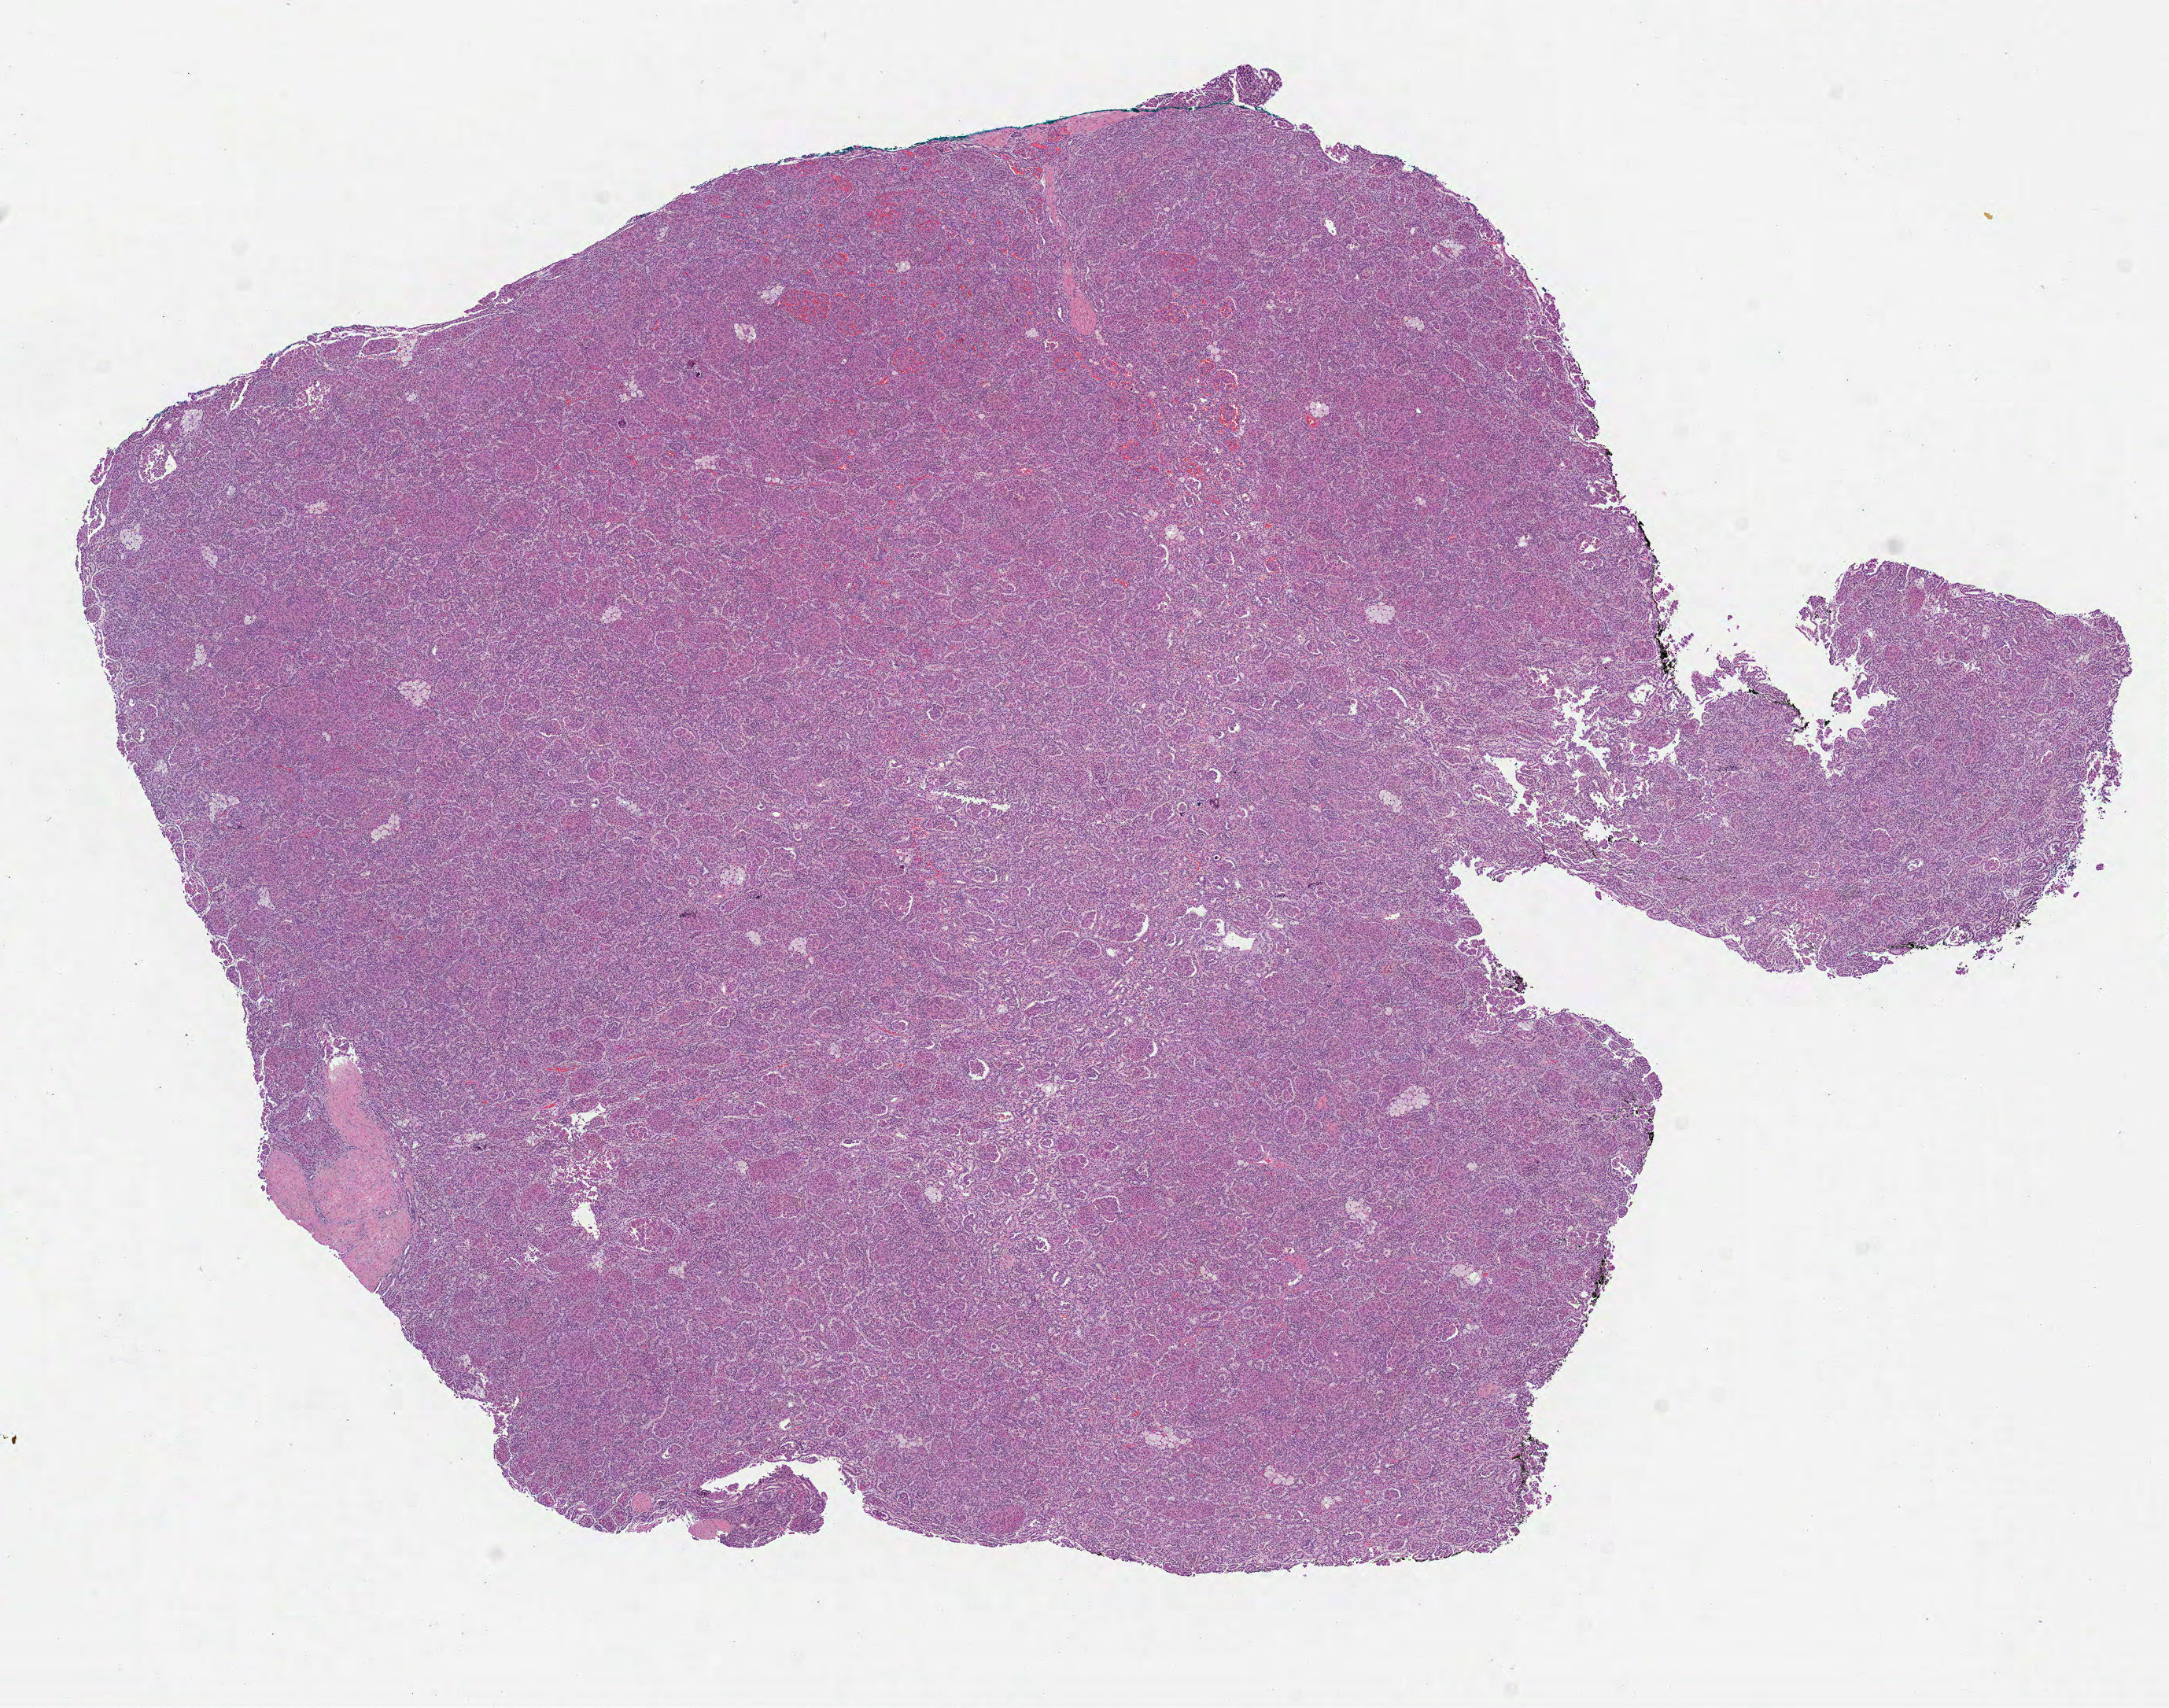
Digitized Hematoxylin and eosin (H&E) stained tissue section (whole slide), low-resolution overview of the scanned area, about 11.1 x 8.8 mm (acquisition: 40x scan). FFPE section. Kidney, primary tumour sample. Female patient; age at initial diagnosis 53 years.
- histologic diagnosis: Papillary adenocarcinoma, NOS
- TNM: T1a NX MX
- AJCC pathologic stage: I (7th edition)
- laterality: right